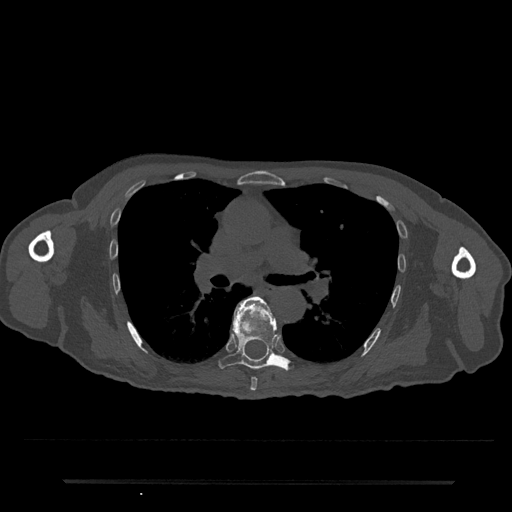
CT including the spine, one axial slice; position 492 of 797 along the scan axis; reconstruction kernel Br40s/3; bone window (W 1800 / L 400 HU); 512 × 512 image matrix, field of view 427 × 427 mm. Male patient, age 74 years. Case-level facts recorded for this patient, not image findings: primary cancer: prostate.
Outlined on this slice (semi-automatically segmented with operator editing):
- T6 vertebra: bounding box (x1, y1, x2, y2) in pixels: (243, 296, 266, 391)
- T7 vertebra: (219, 301, 294, 370)